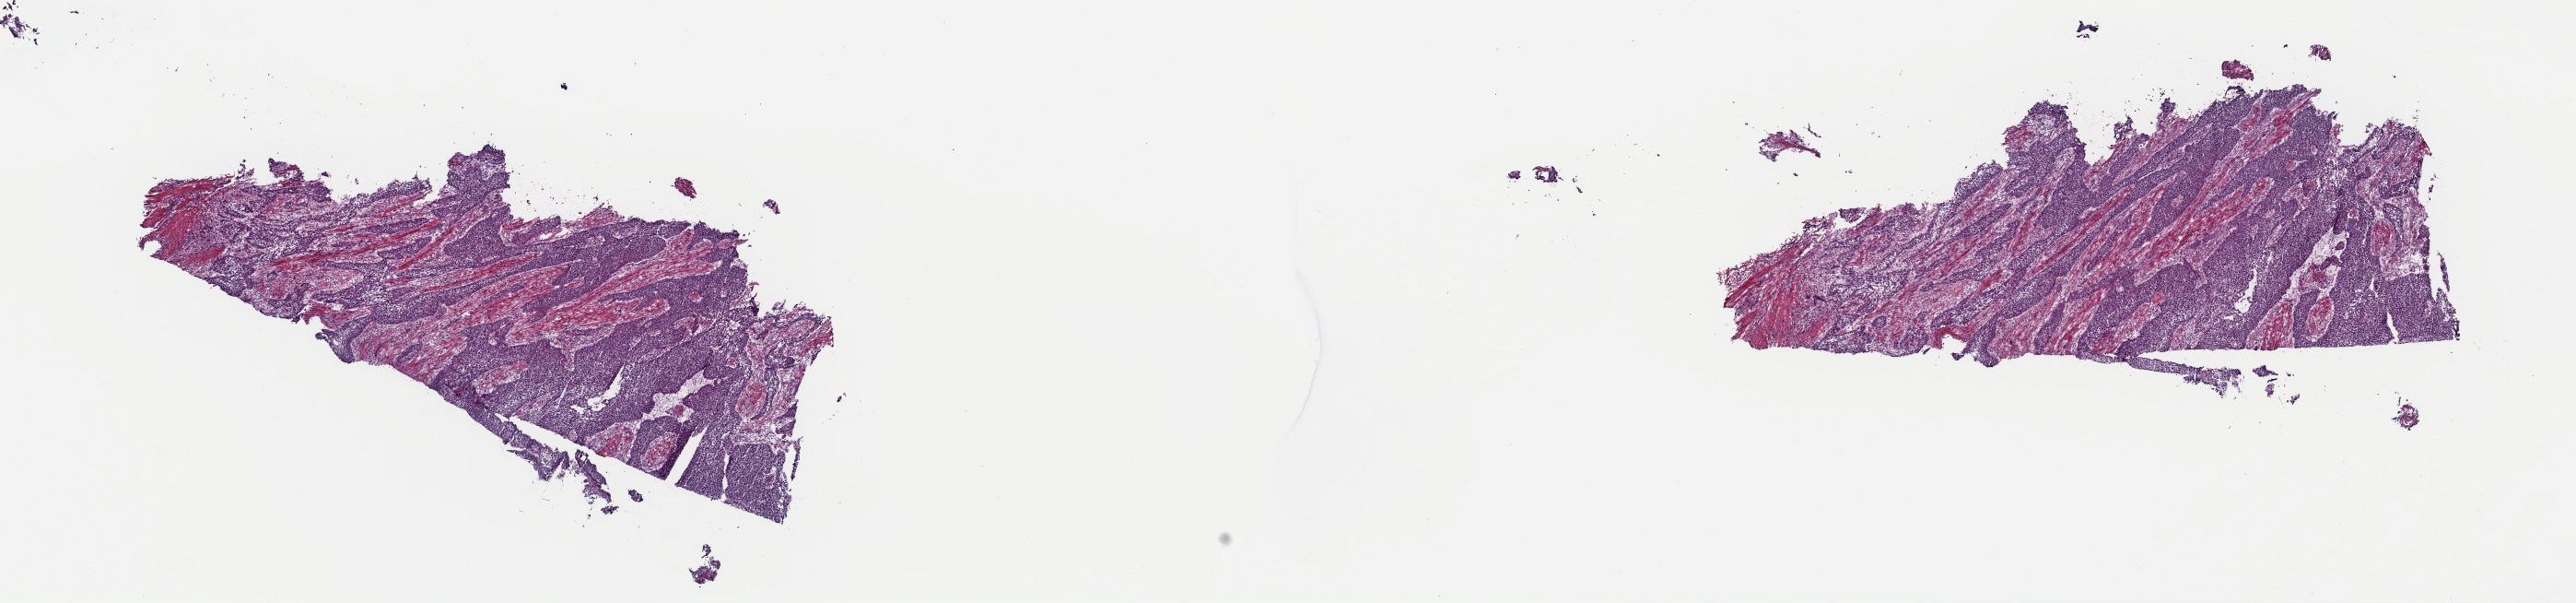
Whole-slide histology image, H&E — a low-resolution overview of the entire scanned area, about 22.1 x 5.2 mm. Frozen section. Primary tumour sample from the bladder. Female, age 63 years at initial diagnosis. Histologic grade: high grade. Pathologist review of this section (percent, as recorded): tumour cells 60%, tumour nuclei 80%, normal cells 0%, stromal cells 34%, necrosis 6%. Inflammatory infiltration, as recorded: lymphocyte infiltration 6%, monocyte infiltration 2%, neutrophil infiltration 3%.
* AJCC pathologic stage: III (7th edition)
* pathologic diagnosis: Transitional cell carcinoma (posterior wall of bladder)
* lymph nodes positive (case pathology): 0 of 19 examined